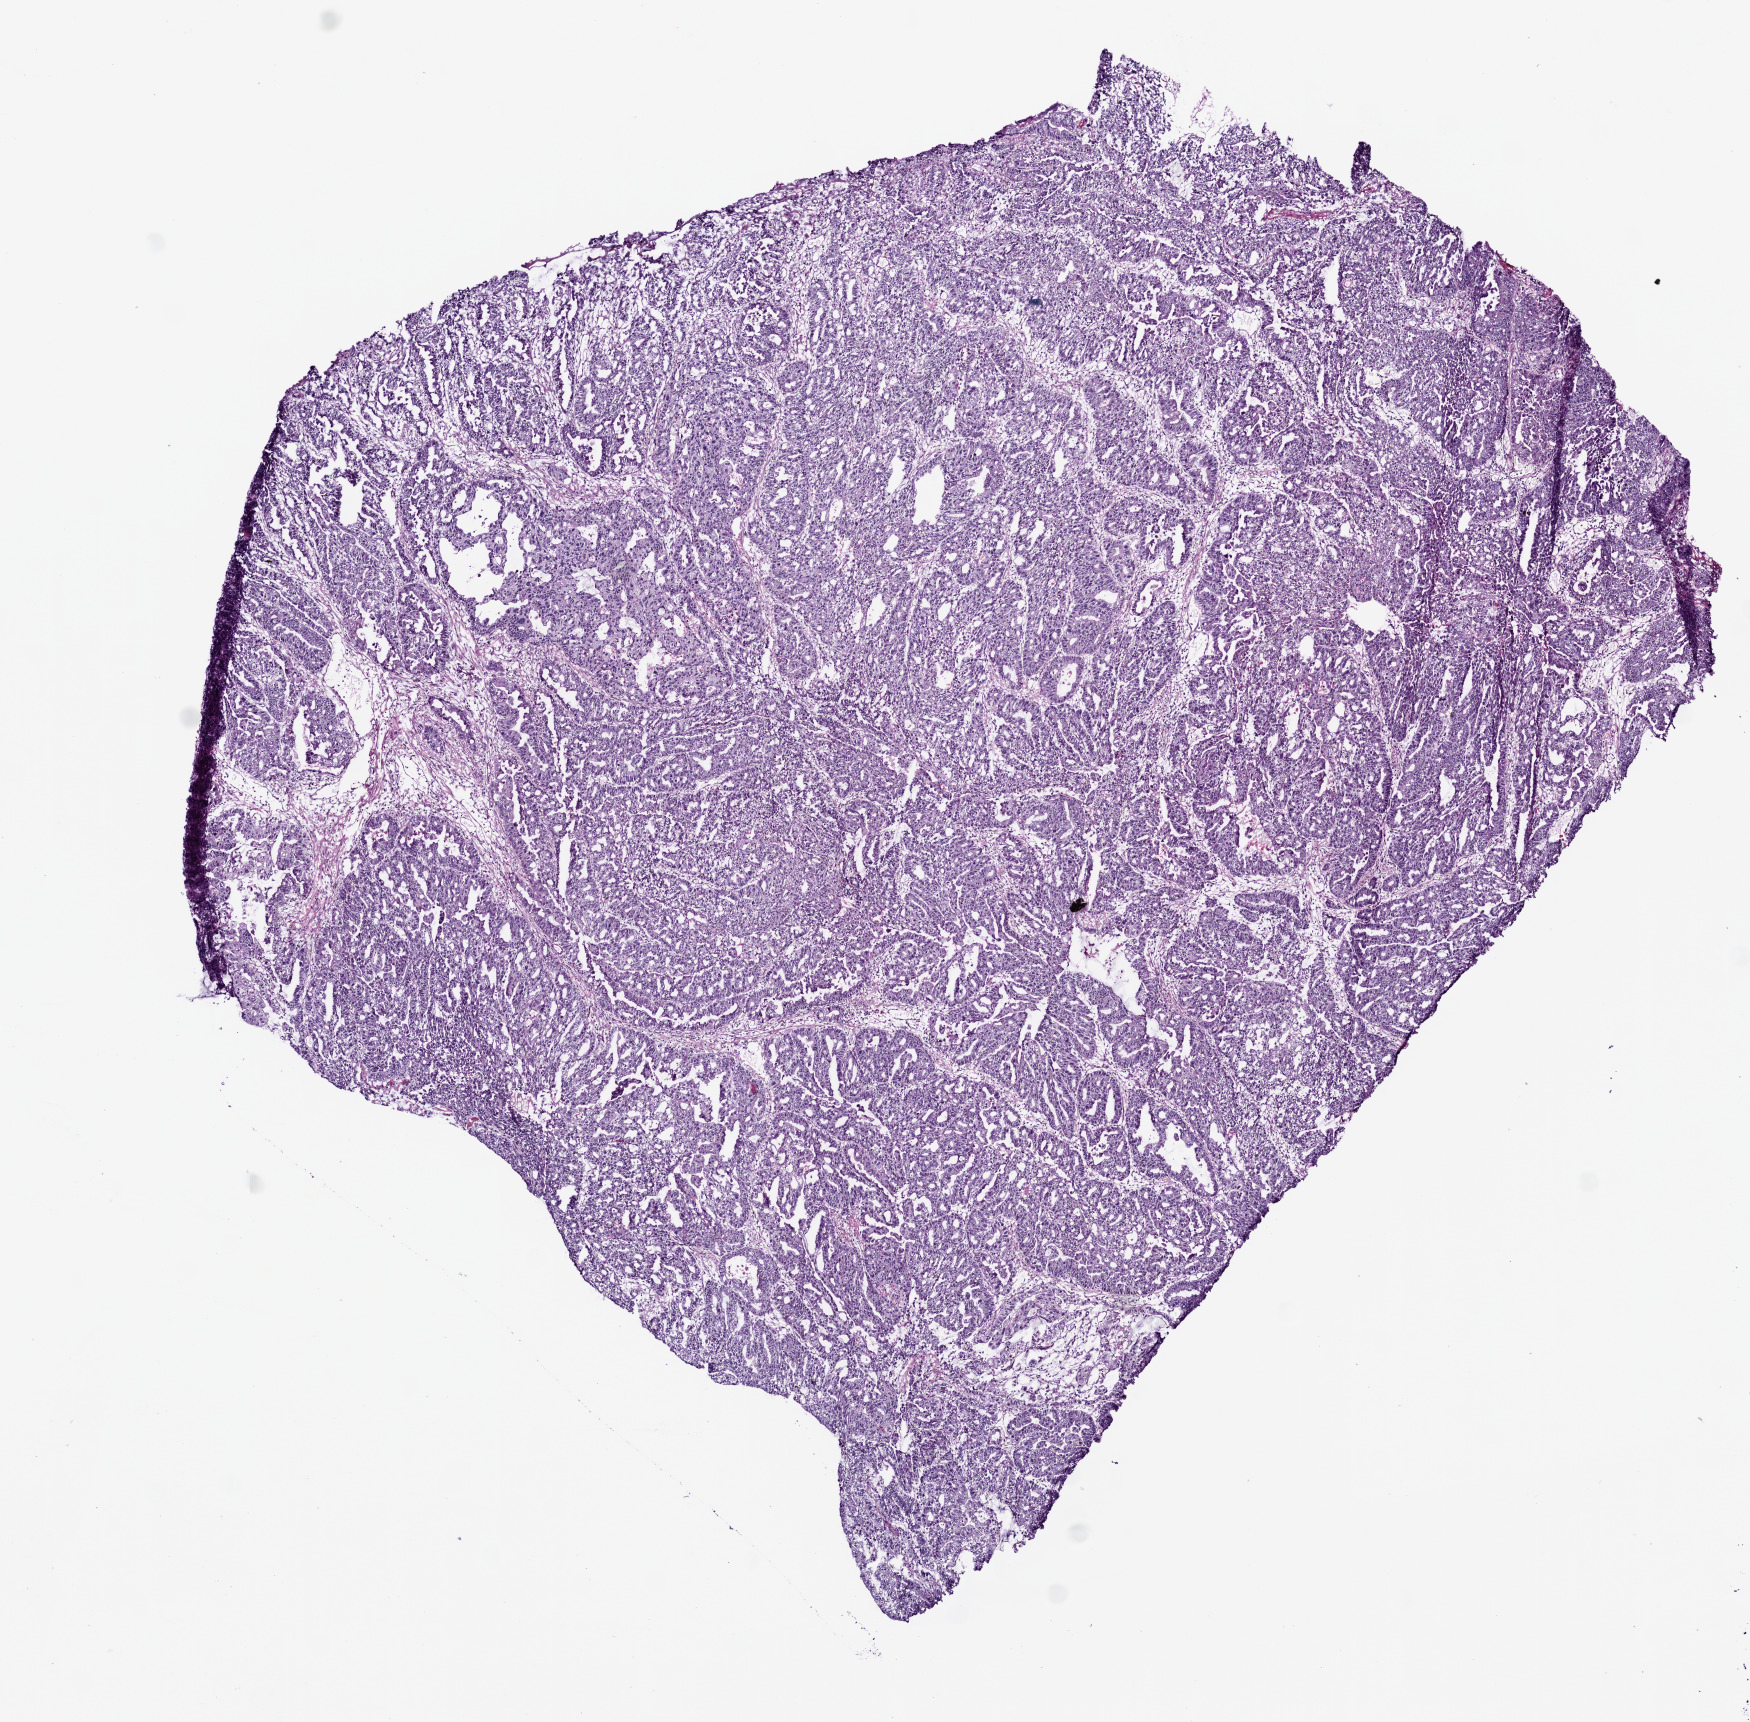
Digitized H&E tissue section (whole slide) — whole scanned area (about 7.0 x 6.9 mm) shown as a low-resolution overview; frozen section from the bottom of the tissue portion; sample: primary tumour, stomach. Female patient; age at initial diagnosis 81 years. Histologic grade: G2 (moderately differentiated). Slide review estimates, as recorded: tumour cells 82%, tumour nuclei 75%, normal cells 3%, stromal cells 10%, necrosis 5%.
TNM: T2a N0 M0. Histologic diagnosis: Adenocarcinoma, intestinal type (cardia, NOS). AJCC pathologic stage: IB (6th edition).